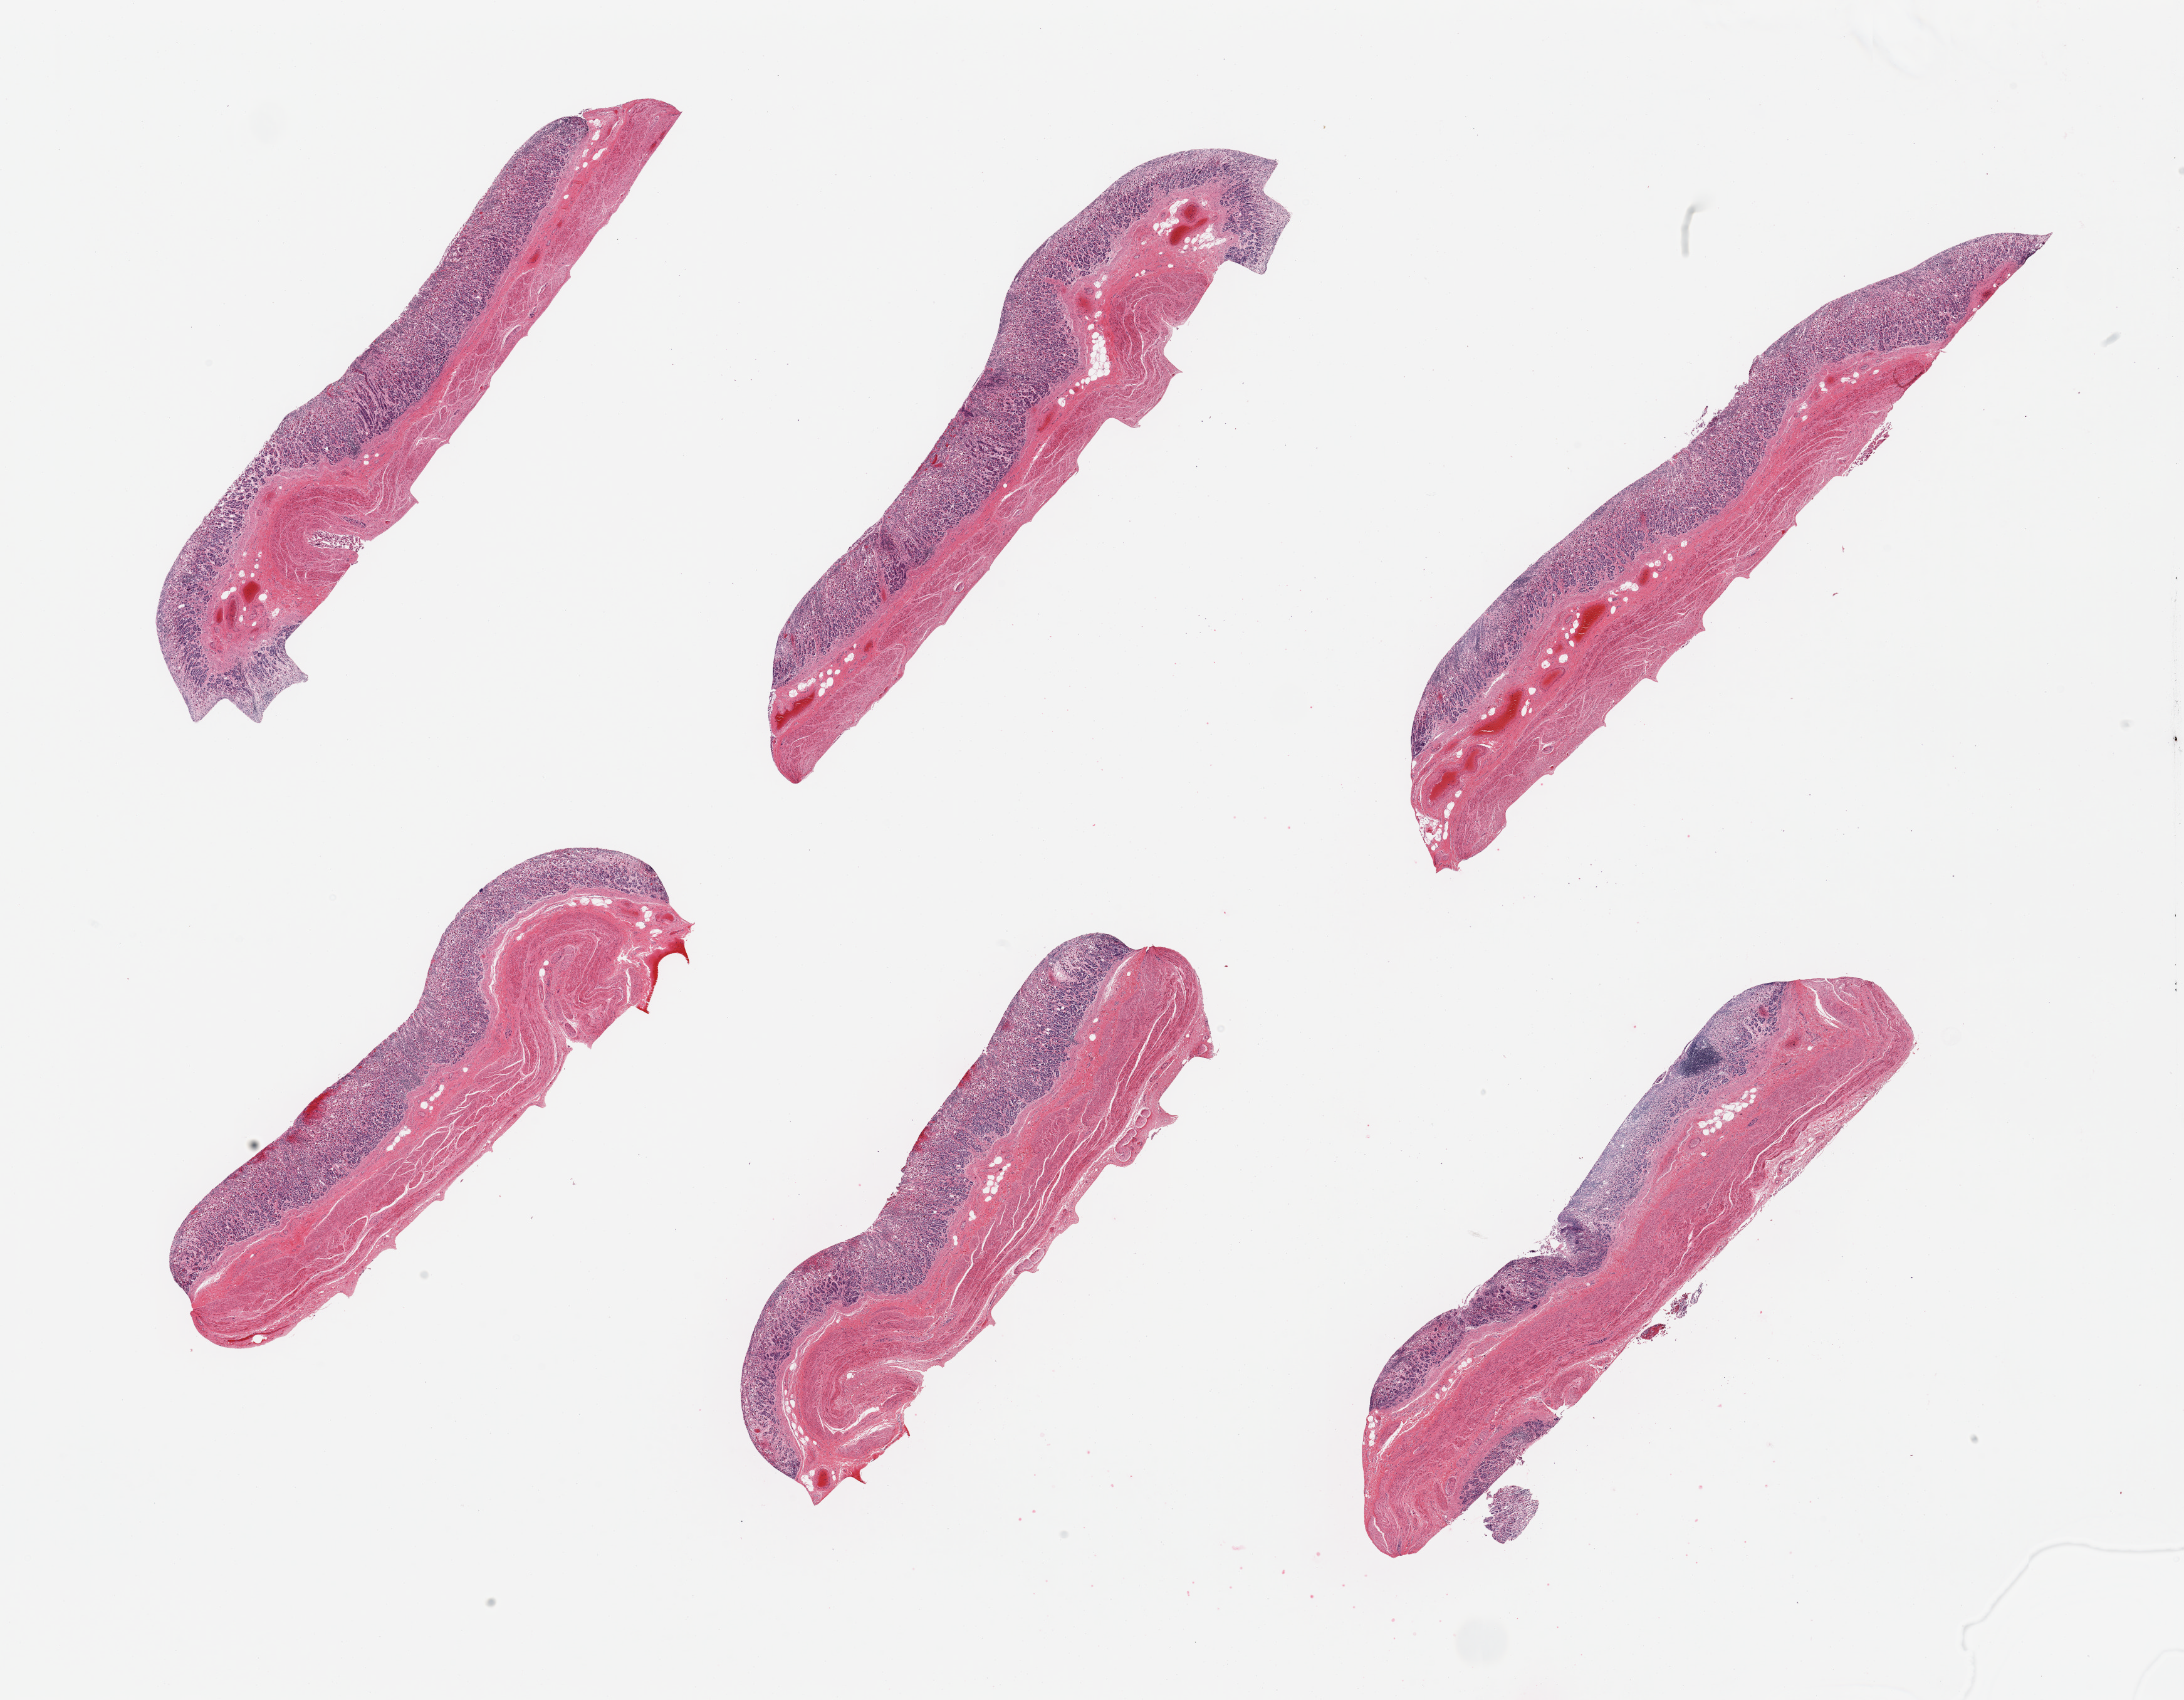
Whole-slide image, haematoxylin and eosin stain, low-resolution overview of the scanned area, about 27.6 x 21.5 mm, PAXgene-fixed, paraffin-embedded tissue, sampled site (target tissue): stomach, donor tissue sample. Female donor.
Review note (as recorded): 6 pieces; chronic gastritis; superficial mucosa autolyzed.